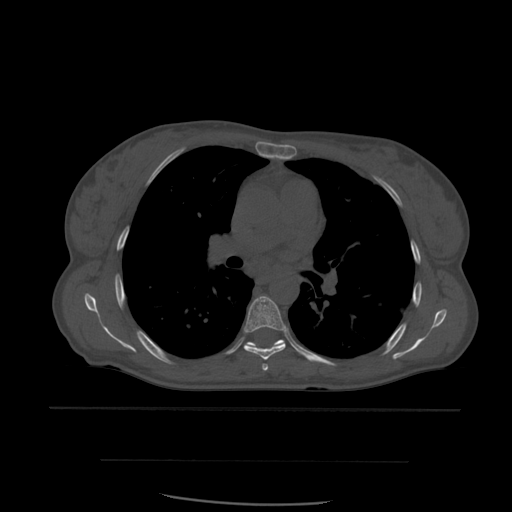
CT including the spine, one axial slice; position 389 of 574 along the scan axis; bone window (W 1800 / L 400 HU); 1.25 mm slice thickness; 512 × 512 image matrix, field of view 392 × 392 mm. Patient age 48 years. Case-level facts recorded for this patient, not image findings: primary cancer: lung.
Structures marked on this image (semi-automatically segmented with operator editing):
- T5 vertebra: bounding box <262,364,269,372> (left, top, right, bottom; pixels)
- T6 vertebra: <244,296,288,361>
- T7 vertebra: <245,340,286,347>